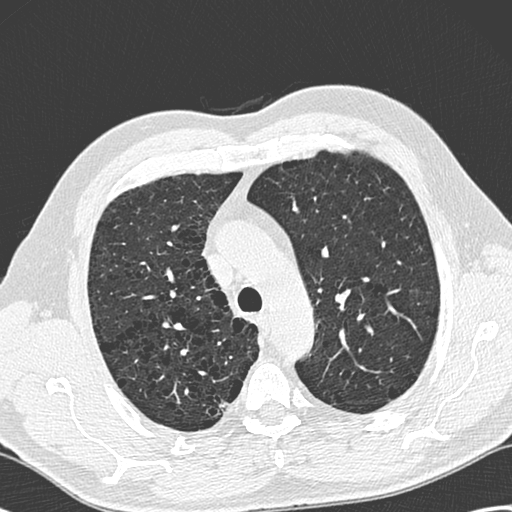
Low-dose screening chest CT, axial slice, baseline annual screen, lung window (W 1500 / L -600 HU), 1.3 mm slice thickness, 120 kVp, slice 63 of 258 in the series, 512 × 512 image matrix, field of view 358 × 358 mm. Male, age 68 years at enrolment. Current smoker at enrolment.
- Expert reader's lesion annotation, bounding box (x1, y1, x2, y2) in pixels: (205, 391, 239, 421).
- Screening reader's record for this exam: no non-calcified nodule ≥4 mm recorded.
- Official screen result: negative screen, minor abnormalities not suspicious for lung cancer.
- Participant outcome: lung cancer diagnosed 777 days after this screen — adenocarcinoma, NOS, right upper lobe, well differentiated (G1), stage IB (AJCC 6th edition), 15 mm at pathology.